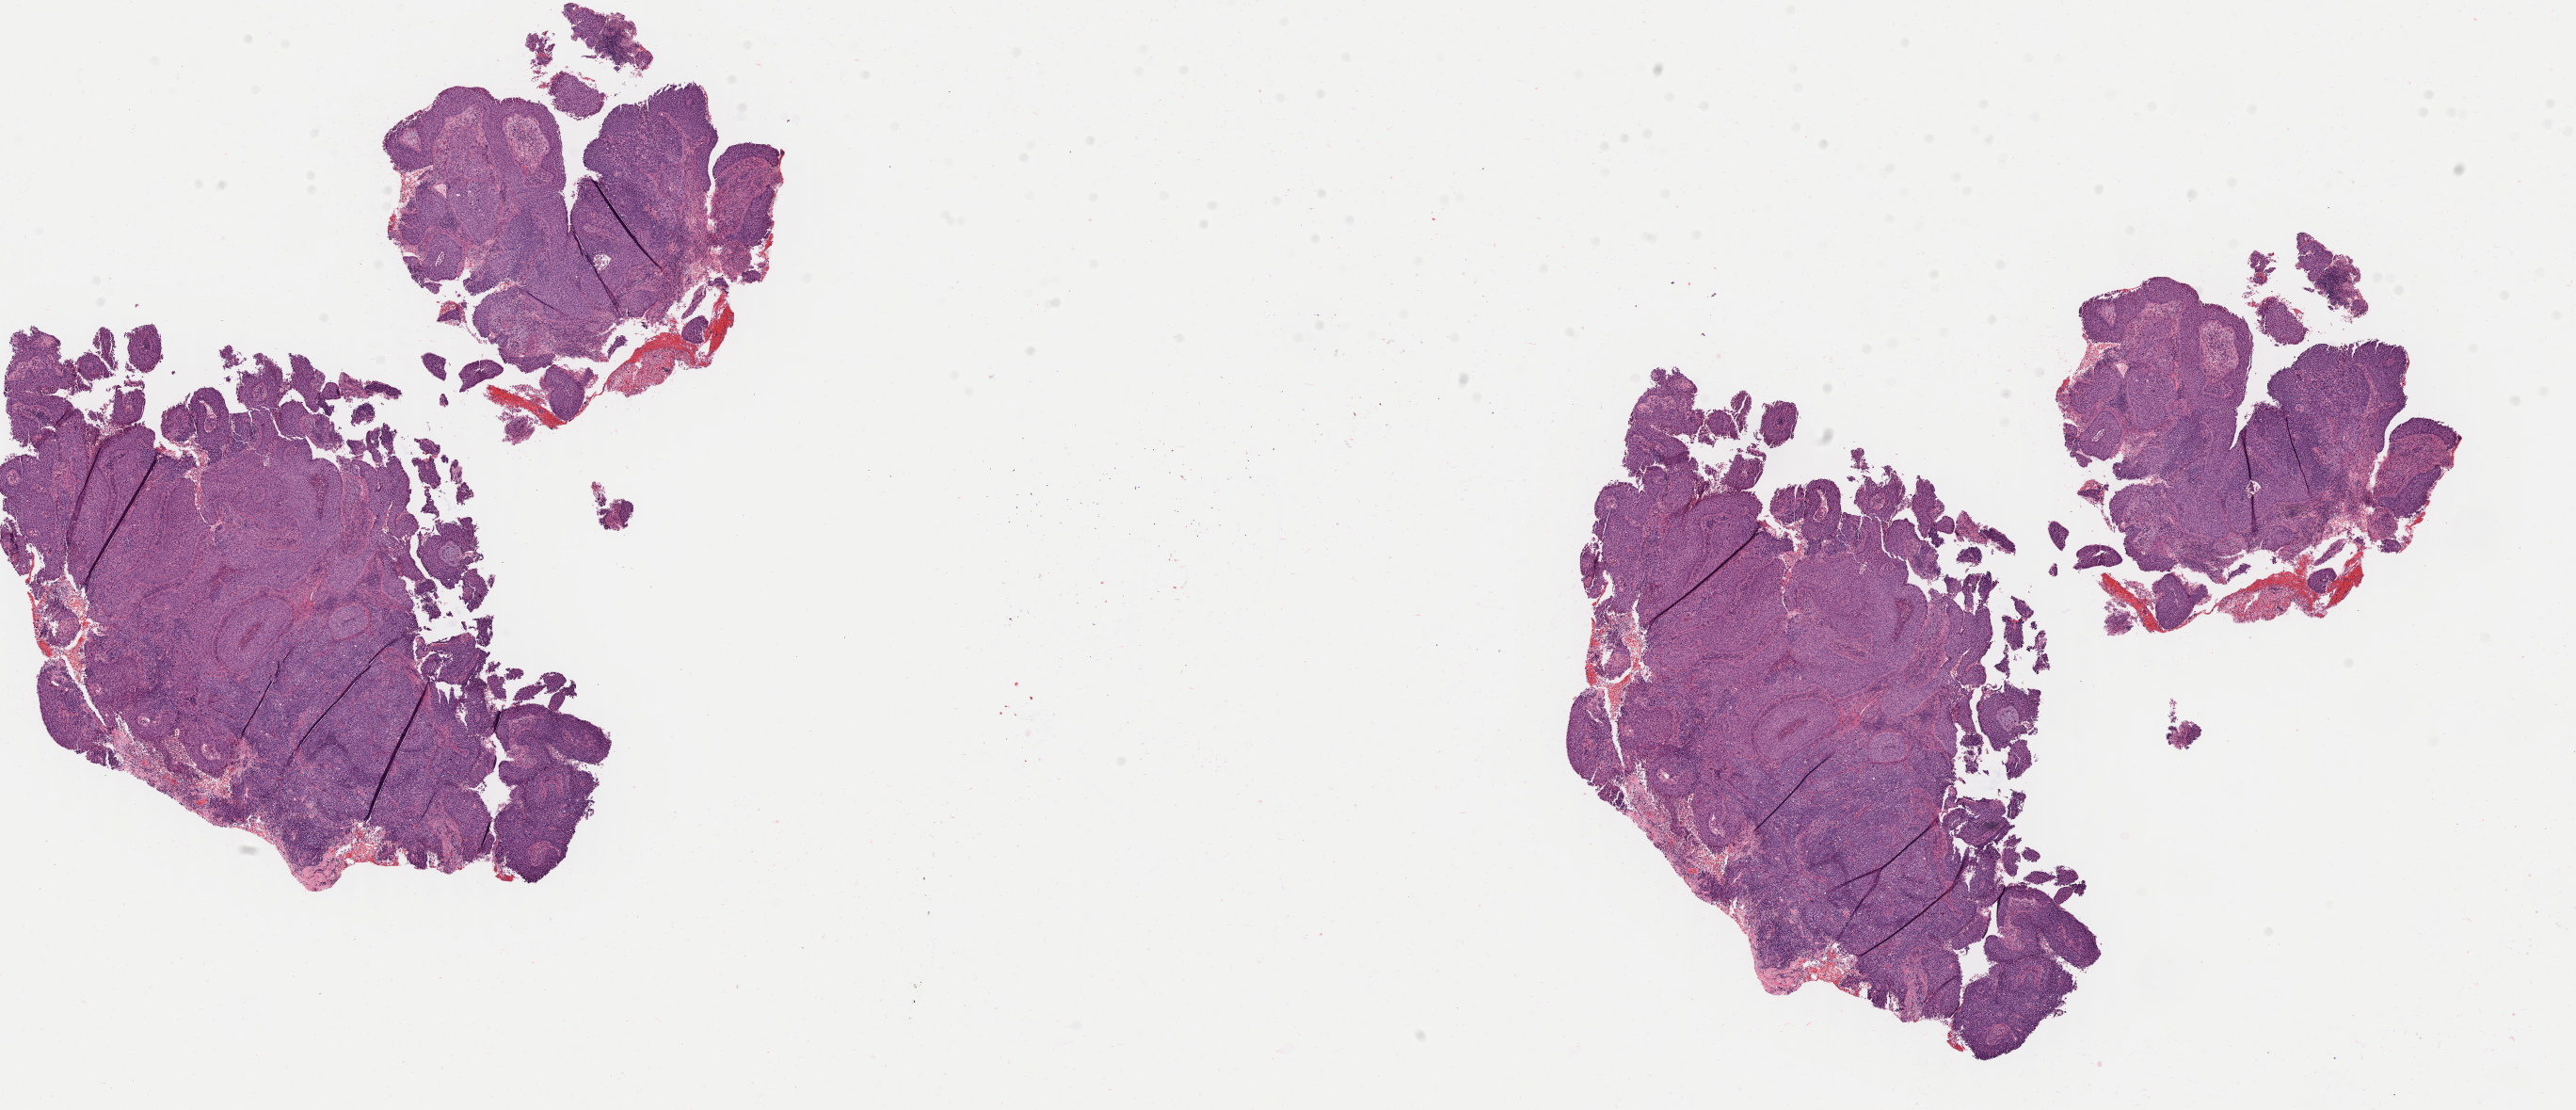
Whole-slide image, H&E stain, low-resolution overview of the scanned area, about 21.8 x 9.4 mm; specimen: tumor tissue; anatomic site: cervix. Female patient, 38 years old.
Diagnosis: Squamous cell carcinoma, large cell, nonkeratinizing, NOS.